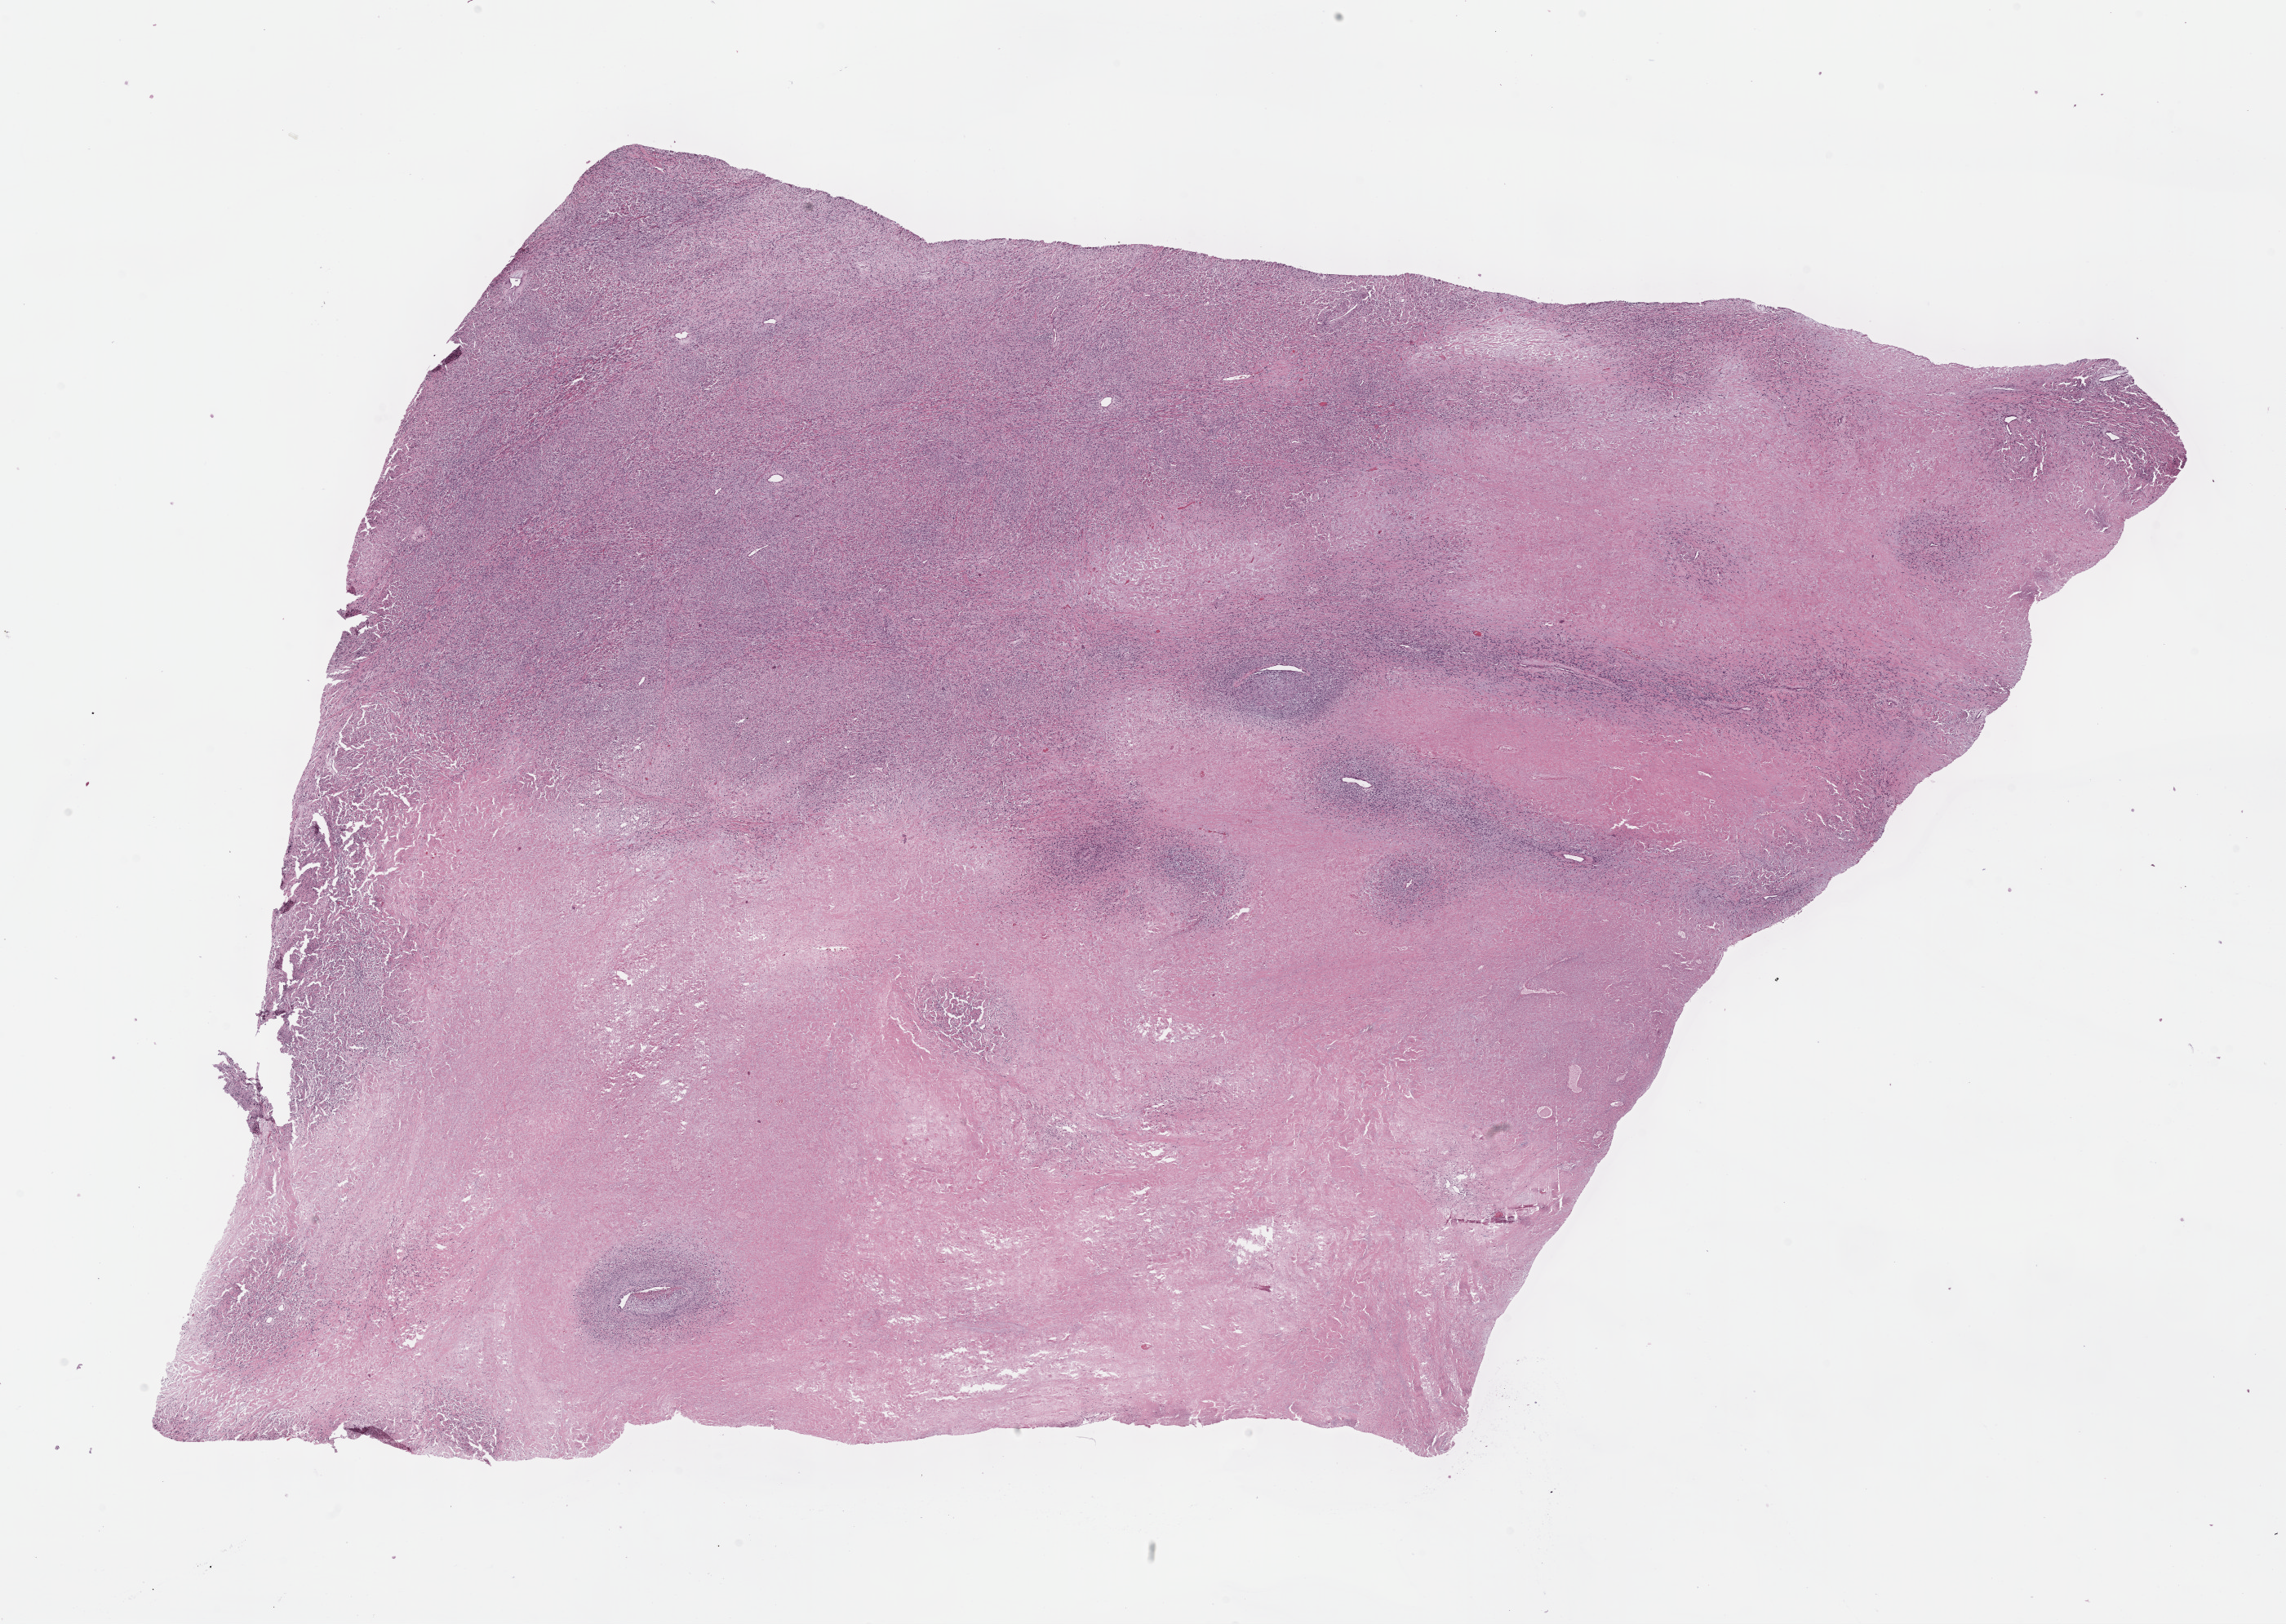
Whole-slide histology image, Hematoxylin and eosin (H&E) stained, shown as a low-resolution overview of the whole scanned area (about 22.7 x 16.1 mm, from a 40x scan); FFPE section; connective, subcutaneous and other soft tissues, primary tumour sample. Female patient; age at initial diagnosis 20 years.
Histologic diagnosis: Malignant peripheral nerve sheath tumor (connective, subcutaneous and other soft tissues of lower limb and hip).